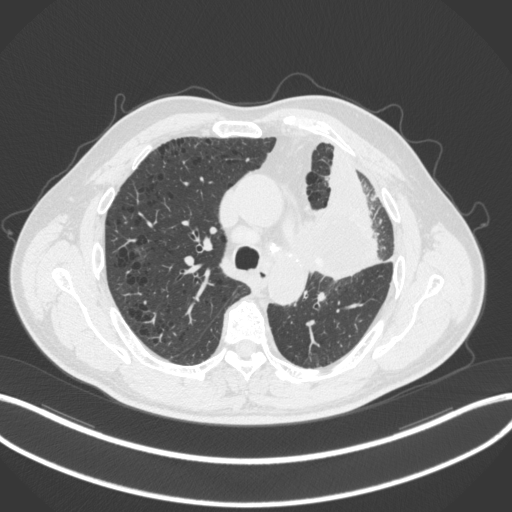
Chest CT, one axial slice. Position 197 of 286 along the scan axis. Reconstruction kernel B31f. 120 kVp. Lung window (W 1500 / L -600 HU). 1 mm slice thickness. 512 × 512 image matrix, field of view 400 × 400 mm. Male patient, age 68 years. Case-level facts recorded for this patient, not image findings: clinical TNM (as recorded): T3 N3 M1.
Structures marked on this image (rectangle marked by the reading radiologist):
- lung tumour (recorded histology: adenocarcinoma): bounding box <292,197,381,285> (left, top, right, bottom; pixels)